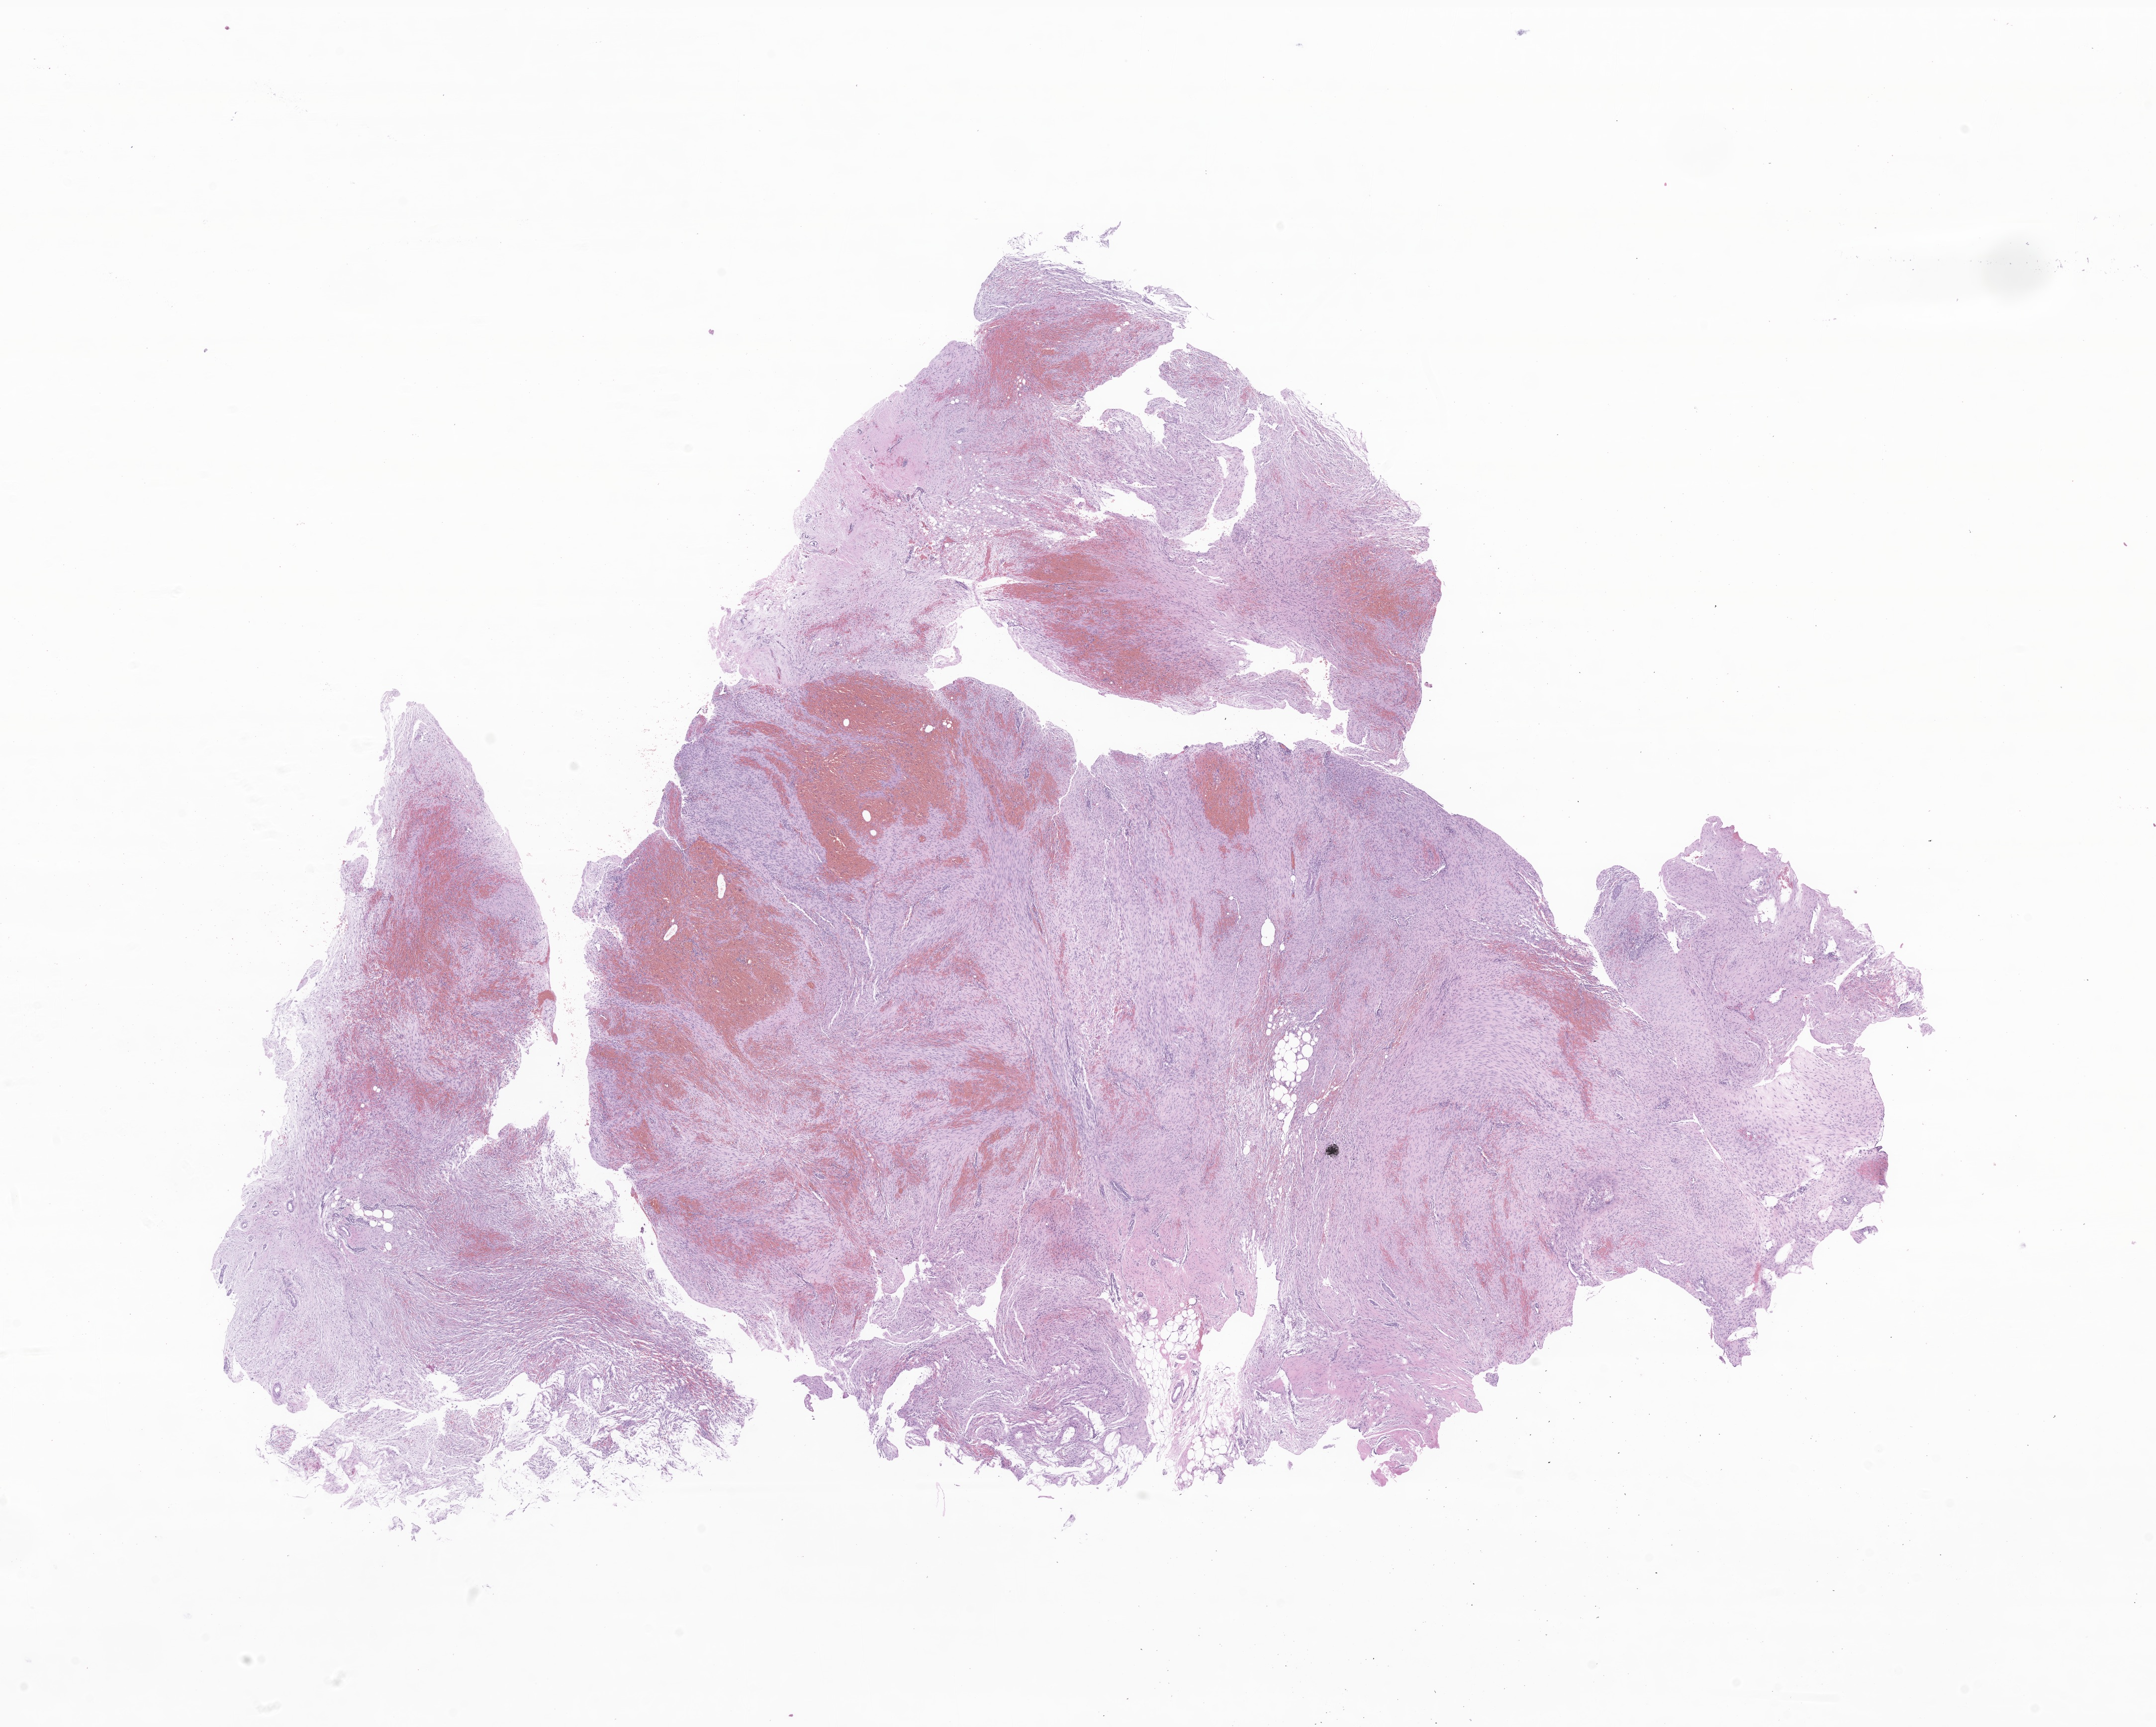
Hematoxylin and eosin (H&E) whole-slide image of tumor tissue from the soft tissue of thorax — a low-resolution overview of the entire scanned area, about 18.3 x 14.6 mm. Formalin-fixed paraffin-embedded section. Female patient, age 164 months (13 years 8 months).
Recorded diagnosis: Aggressive fibromatosis.